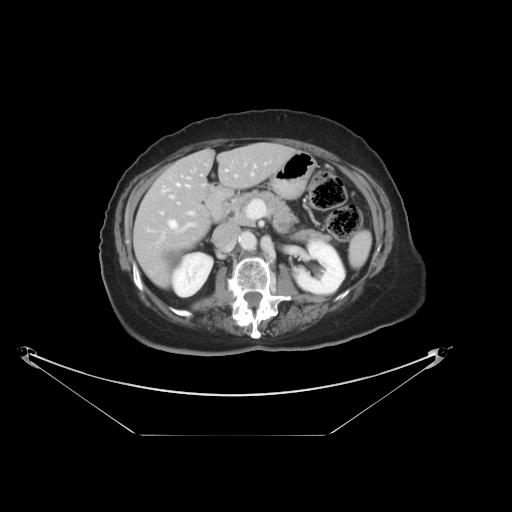
Contrast-enhanced abdominal CT, one axial slice. Position 17 of 36 along the scan axis. Reconstruction kernel STANDARD. 120 kVp. Soft-tissue window (W 400 / L 40 HU). 5 mm slice thickness. 512 × 512 image matrix, field of view 500 × 500 mm. Female patient, age 70 years. Case-level facts recorded for this patient, not image findings: diagnosis: colorectal cancer liver metastases, imaged before liver resection; multiple liver metastases: no; largest metastasis: 2.5 cm; disease in both lobes: no.
Outlined on this slice (manually delineated by an expert):
- hepatic veins: bounding box <169,166,256,229> (left, top, right, bottom; pixels)
- liver: <136,144,293,286>
- planned liver remnant (the part of the liver to remain after resection): <136,144,293,286>
- portal vein (with intrahepatic branches): <161,173,254,229>